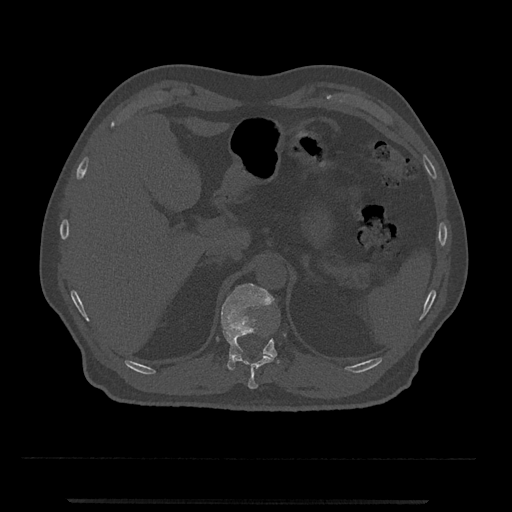
CT including the spine, one axial slice. Position 431 of 797 along the scan axis. Bone window (W 1800 / L 400 HU). 0.5 mm slice thickness. 512 × 512 image matrix, field of view 419 × 419 mm. Patient: male, 63 years. From the clinical record (not read from this slice): primary cancer: prostate.
Outlined on this slice (semi-automatically segmented with operator editing):
- T11 vertebra: bounding box <233,354,274,389> (left, top, right, bottom; pixels)
- T12 vertebra: <221,283,280,370>